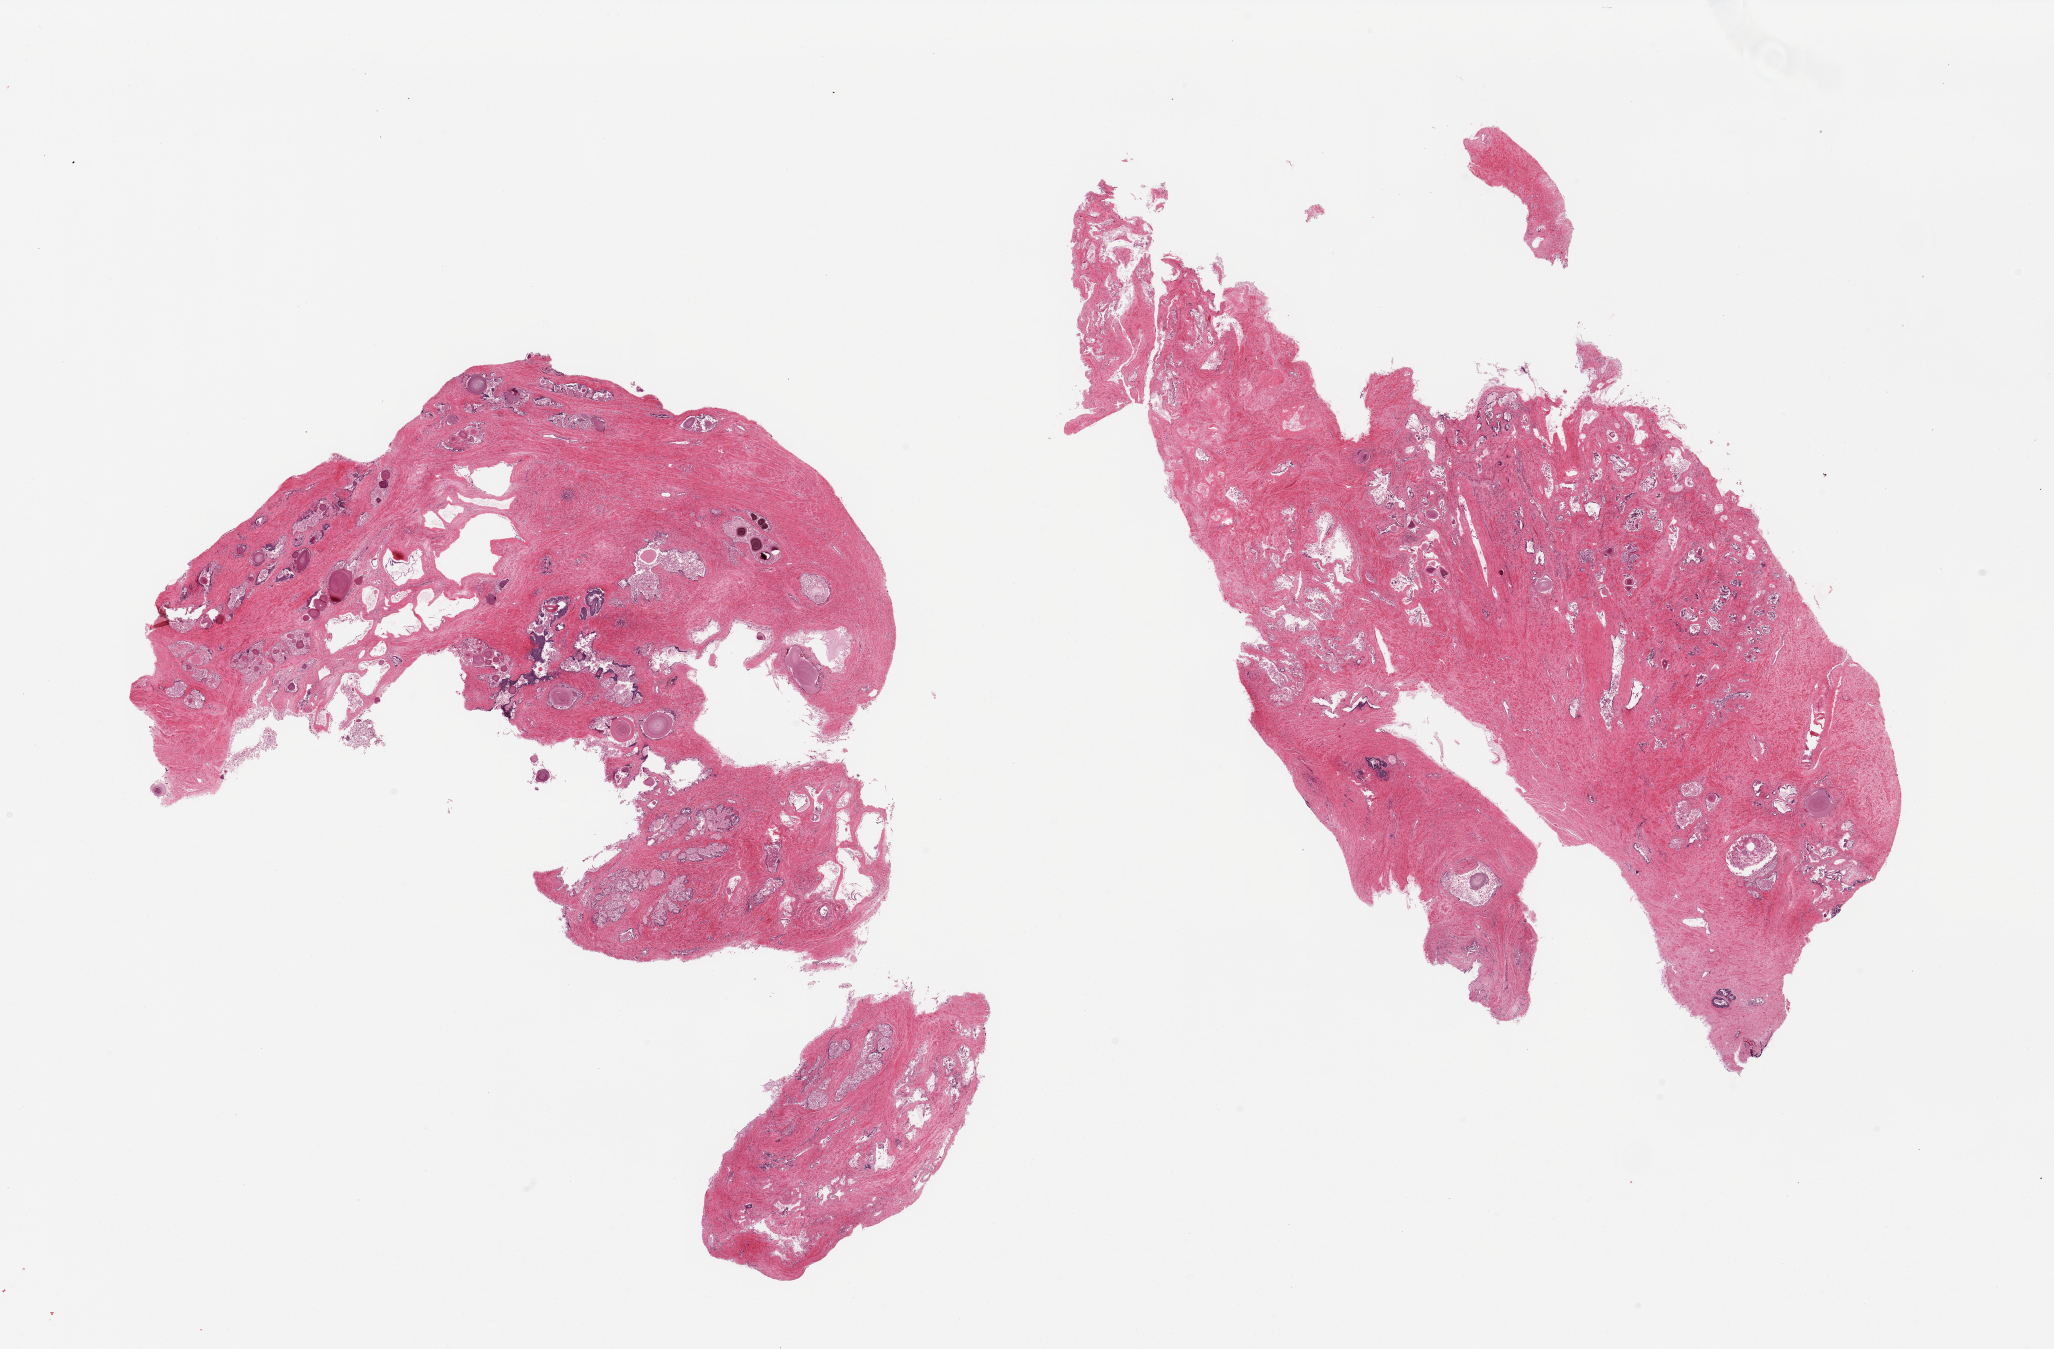
Whole-slide image, H&E stain, shown as a low-resolution overview of the whole scanned area (about 32.5 x 21.3 mm). PAXgene-fixed, paraffin-embedded tissue. Section of prostate (target tissue). Donor tissue sample. Male donor.
Reviewer comment on this tissue sample: 2 pieces, basal cell hyperplasia, numerous corpora amylacea, glands largely sloughed.